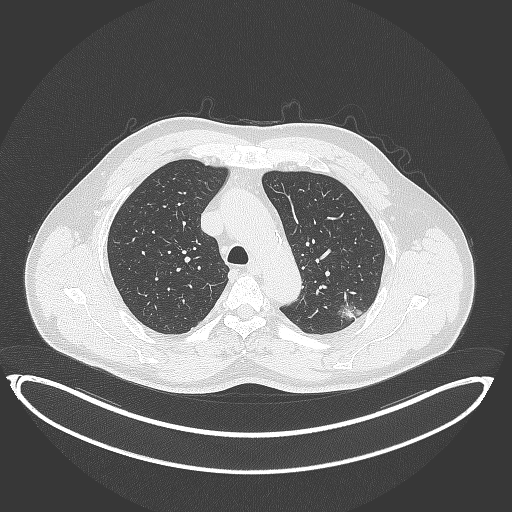
Chest CT, one axial slice; position 268 of 399 along the scan axis; lung window (W 1500 / L -600 HU); 1 mm slice thickness; 512 × 512 image matrix, field of view 469 × 469 mm. Patient: male, 58 years. From the clinical record (not read from this slice): clinical TNM (as recorded): T1c N0 M0.
Outlined on this slice (bounding box drawn by a radiologist):
- lung tumour (recorded histology: adenocarcinoma): bounding box <336,296,365,323> (left, top, right, bottom; pixels)